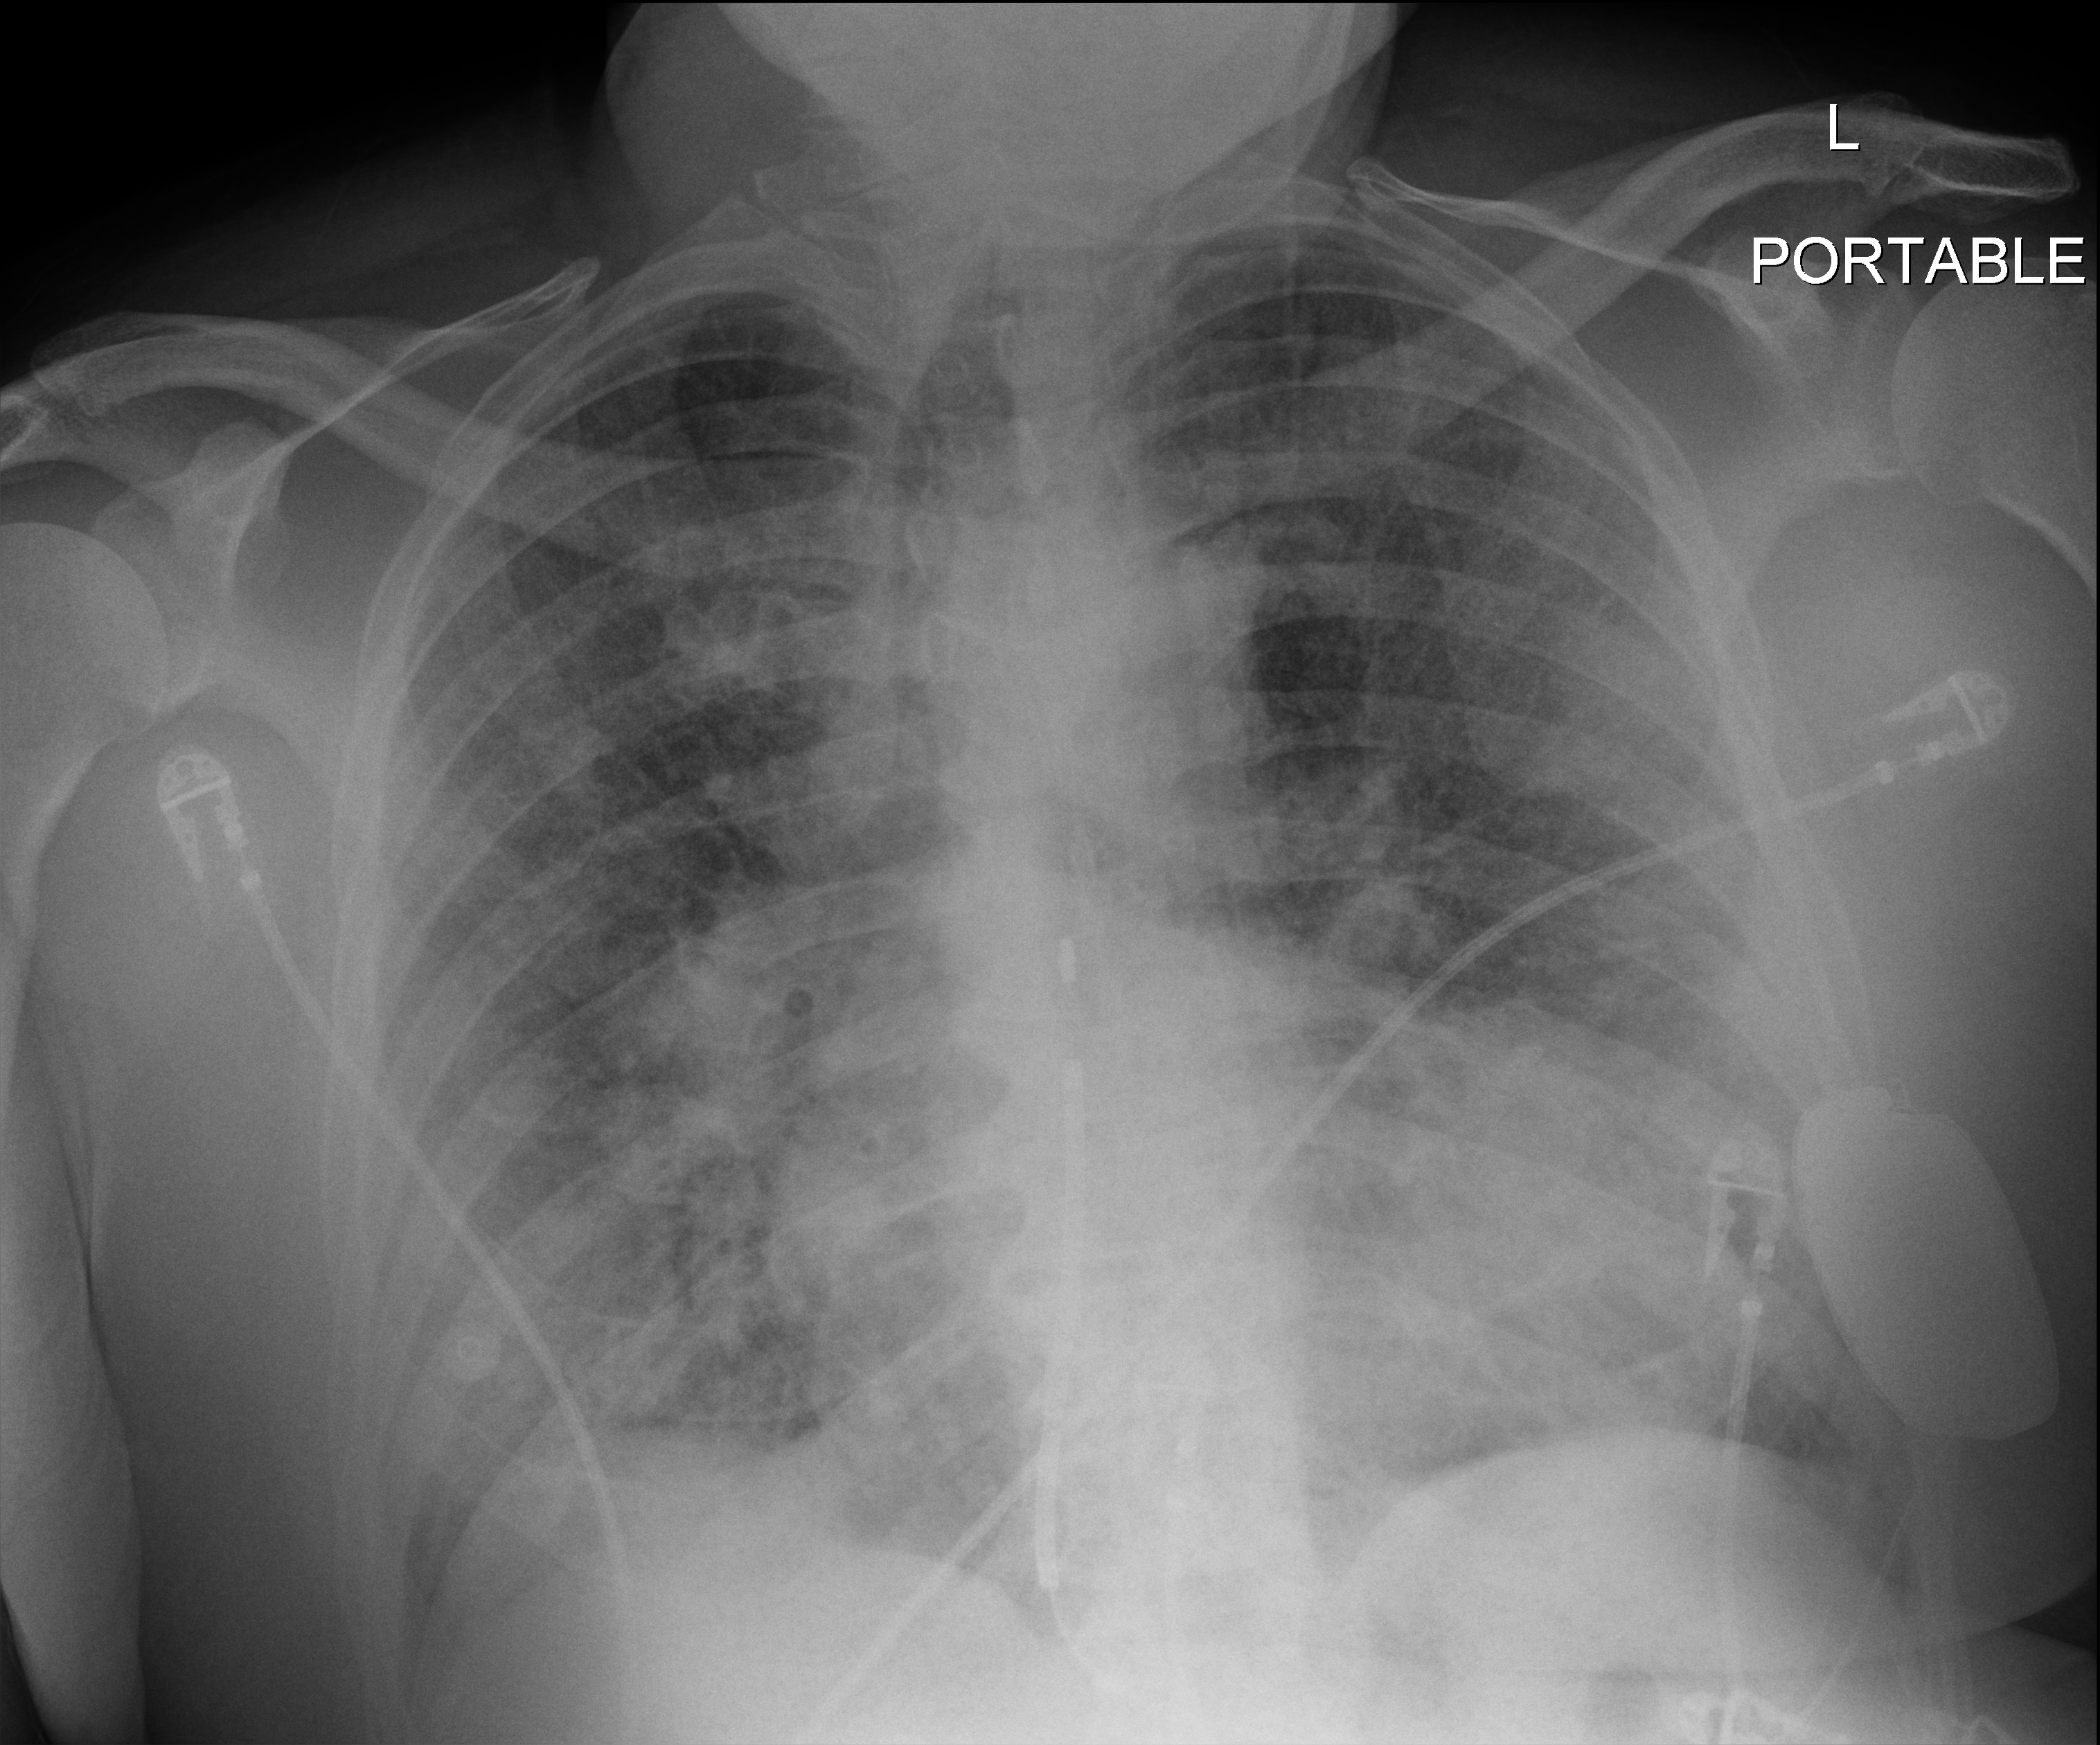
Chest X-ray (portable), anteroposterior (AP) projection. Patient hospitalised with COVID-19; male, aged 60–74 years.
Admission-level facts for this patient (not findings on this image; timing relative to this image not recorded):
- smoking status (admission record): never